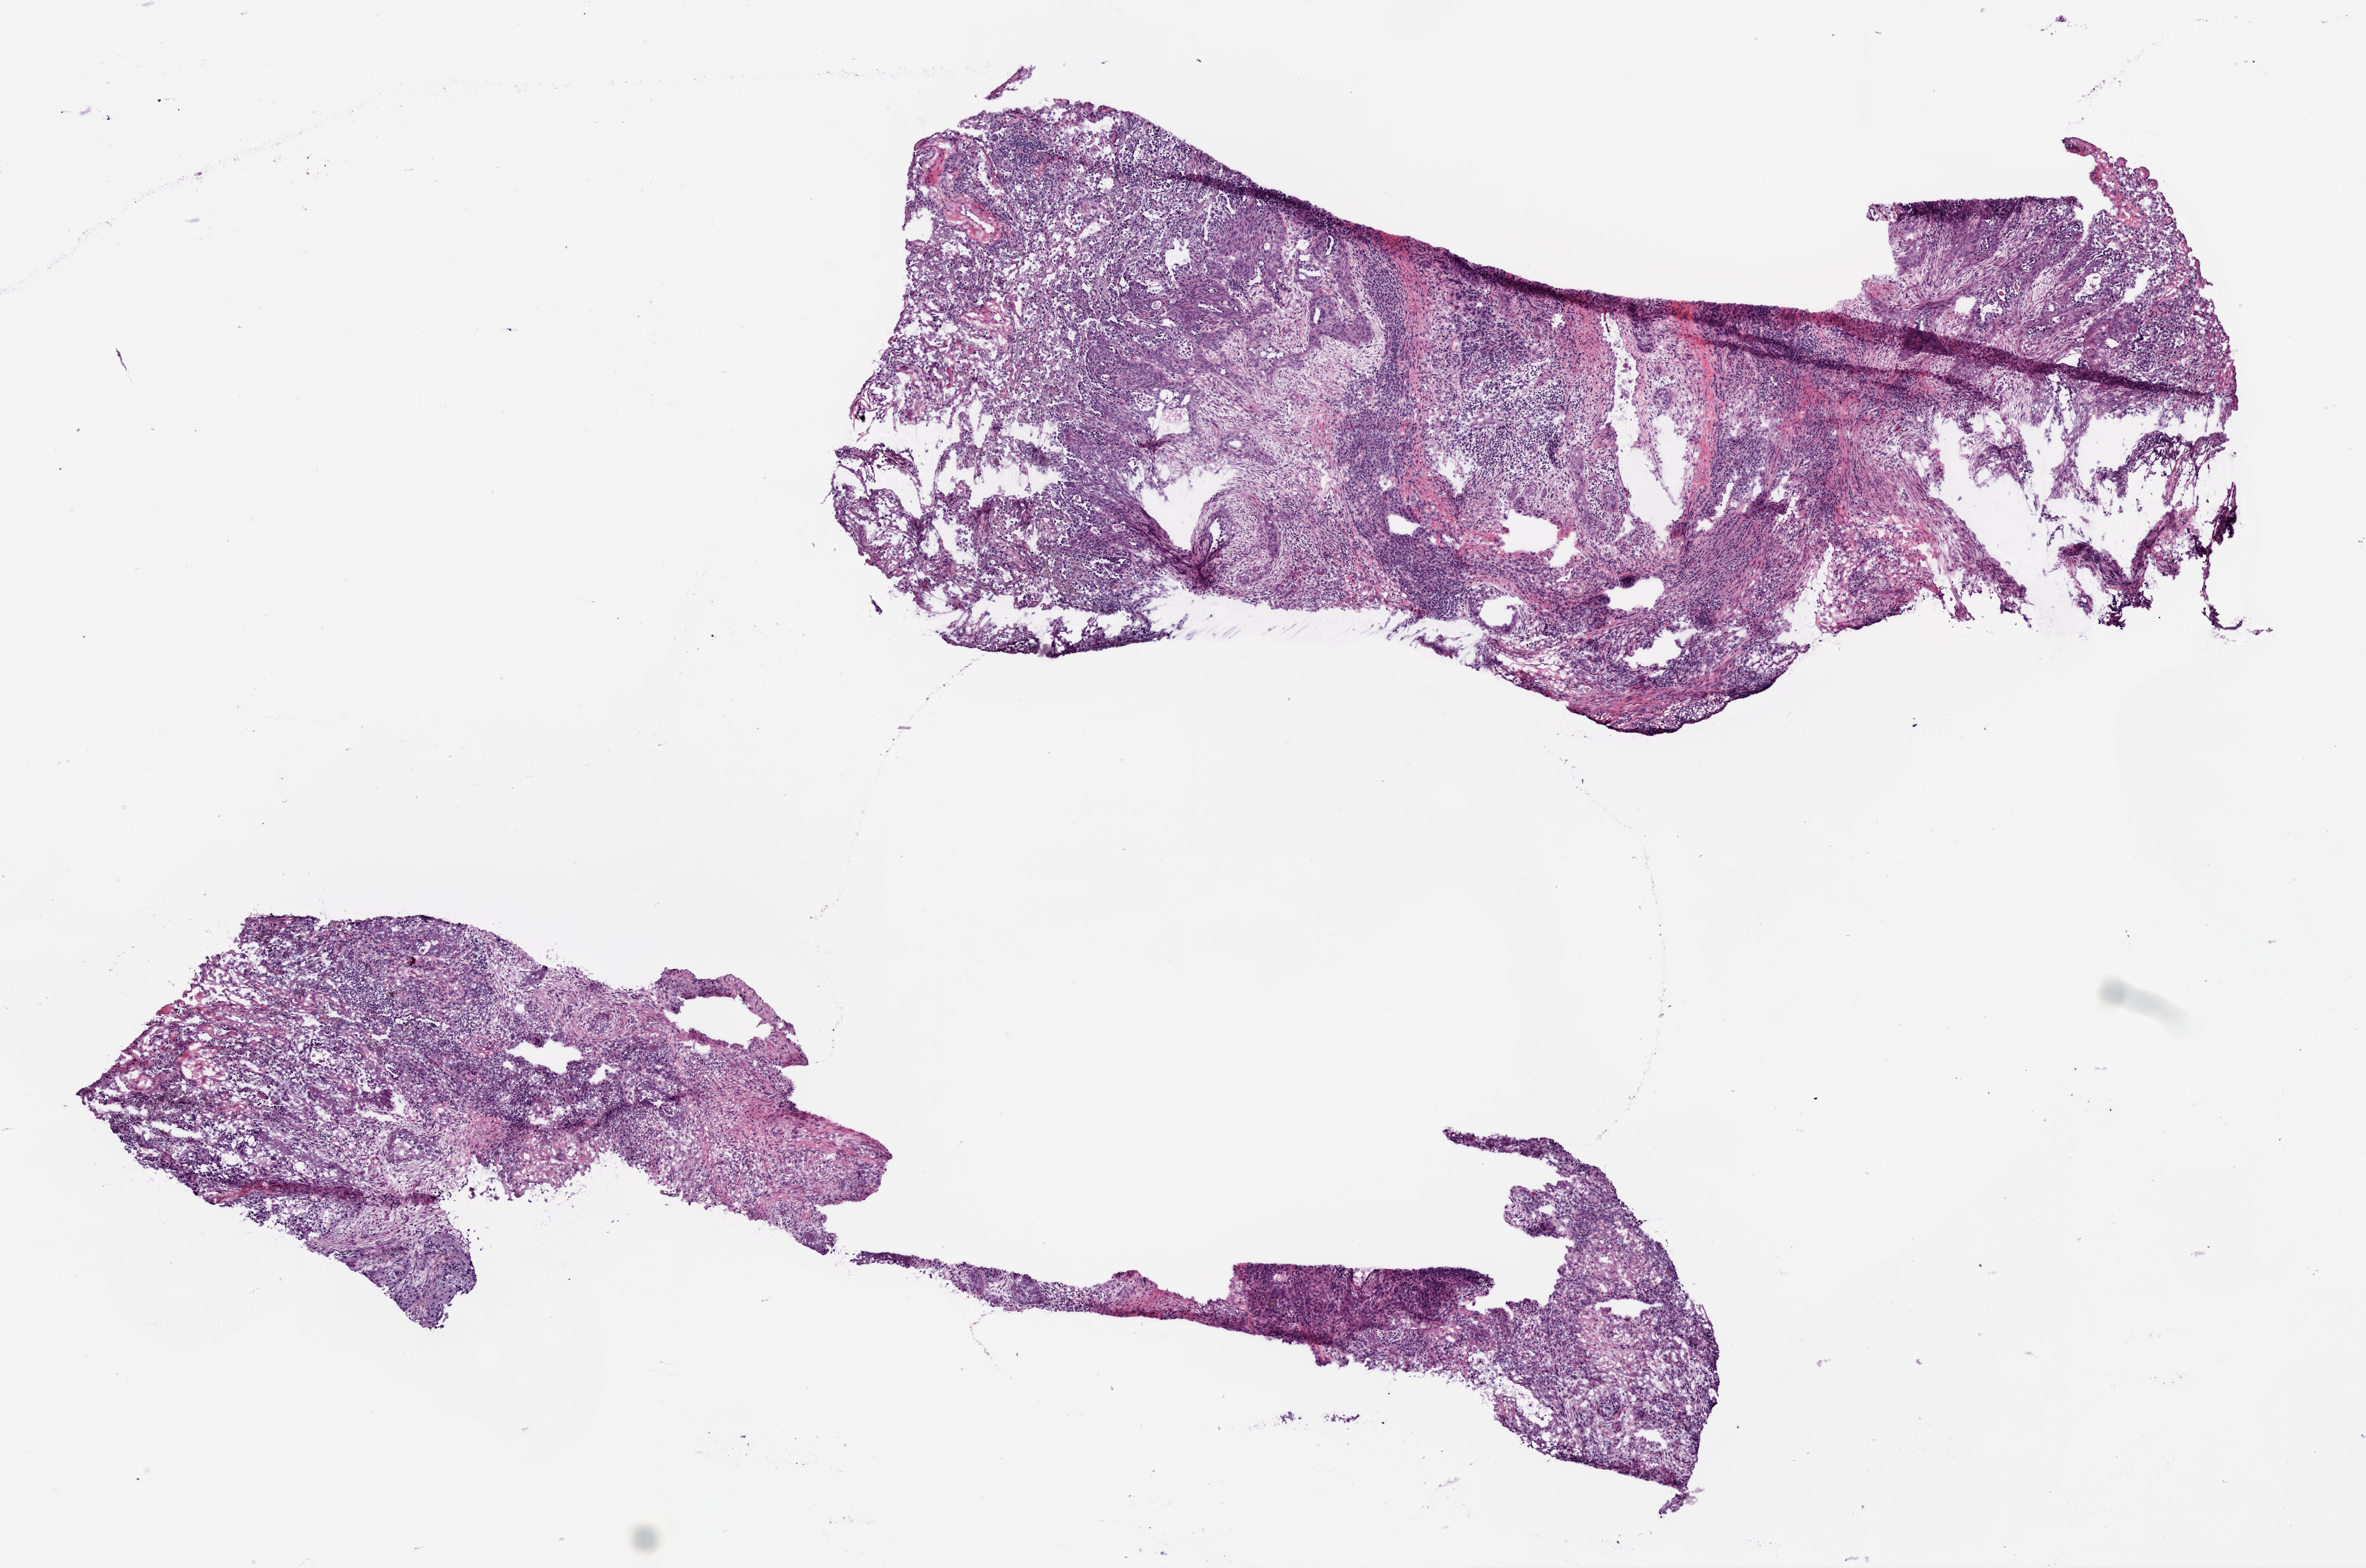
Whole-slide histology image, H&E-stained — shown as a low-resolution overview of the whole scanned area (about 8.0 x 5.3 mm), frozen section from the bottom of the tissue portion, sample: primary tumour, lung. Female patient; age at initial diagnosis 62 years. Pathologist review of this section (percent, as recorded): tumour cells 72%, tumour nuclei 70%, normal cells 10%, stromal cells 15%, necrosis 3%.
AJCC pathologic stage: IA. Diagnosis: Squamous cell carcinoma, NOS (lower lobe, lung). TNM: T1 N0 M0.